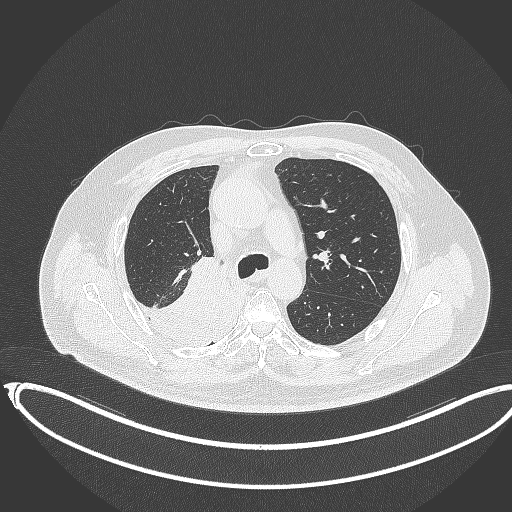
Chest CT, one axial slice. Position 242 of 403 along the scan axis. Reconstruction kernel B70f. 120 kVp. Lung window (W 1500 / L -600 HU). 1 mm slice thickness. 512 × 512 image matrix, field of view 436 × 436 mm. Male patient, age 68 years. From the clinical record (not read from this slice): clinical TNM (as recorded): T2a N0 M0.
Structures marked on this image (rectangle marked by the reading radiologist):
- lung tumour (recorded histology: adenocarcinoma): bounding box [x1, y1, x2, y2] px = [119, 249, 242, 350]